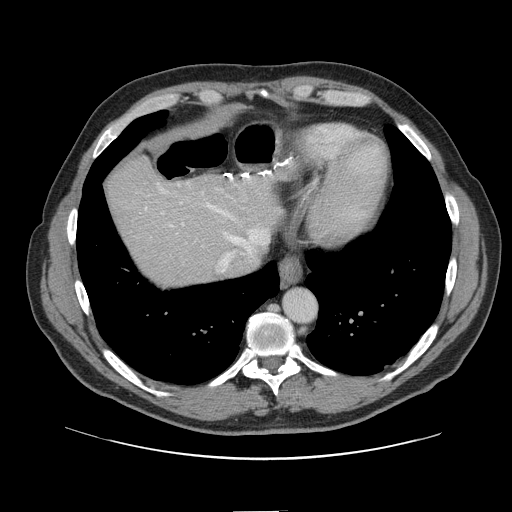
Contrast-enhanced abdominal CT, one axial slice. Slice 128 of 161 in the series (ordered by position). Soft-tissue window (W 400 / L 40 HU). 512 × 512 image matrix, field of view 412 × 412 mm. Male patient, age 66 years. From the clinical record (not read from this slice): diagnosis: colorectal cancer liver metastases, imaged before liver resection; multiple liver metastases: no.
Outlined on this slice (expert manual segmentation):
- hepatic veins: bounding box [x1, y1, x2, y2] px = [146, 178, 270, 273]
- liver: [107, 158, 281, 287]
- planned liver remnant (the part of the liver to remain after resection): [107, 159, 280, 285]